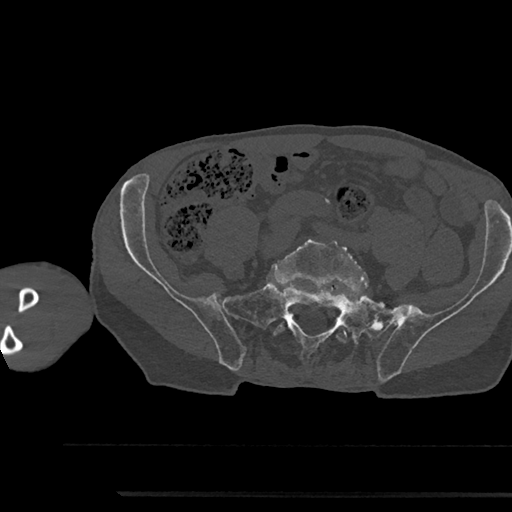
CT including the spine, one axial slice; slice 313 of 797 in the series (ordered by position); reconstruction kernel Br40s/3; 120 kVp; bone window (W 1800 / L 400 HU); 0.5 mm slice thickness; 512 × 512 image matrix, field of view 367 × 367 mm. Male patient, age 79 years. From the clinical record (not read from this slice): primary cancer: prostate.
Outlined on this slice (semi-automatic segmentation, software-assisted and operator-edited):
- L5 vertebra: bounding box [x1, y1, x2, y2] px = [273, 235, 368, 343]